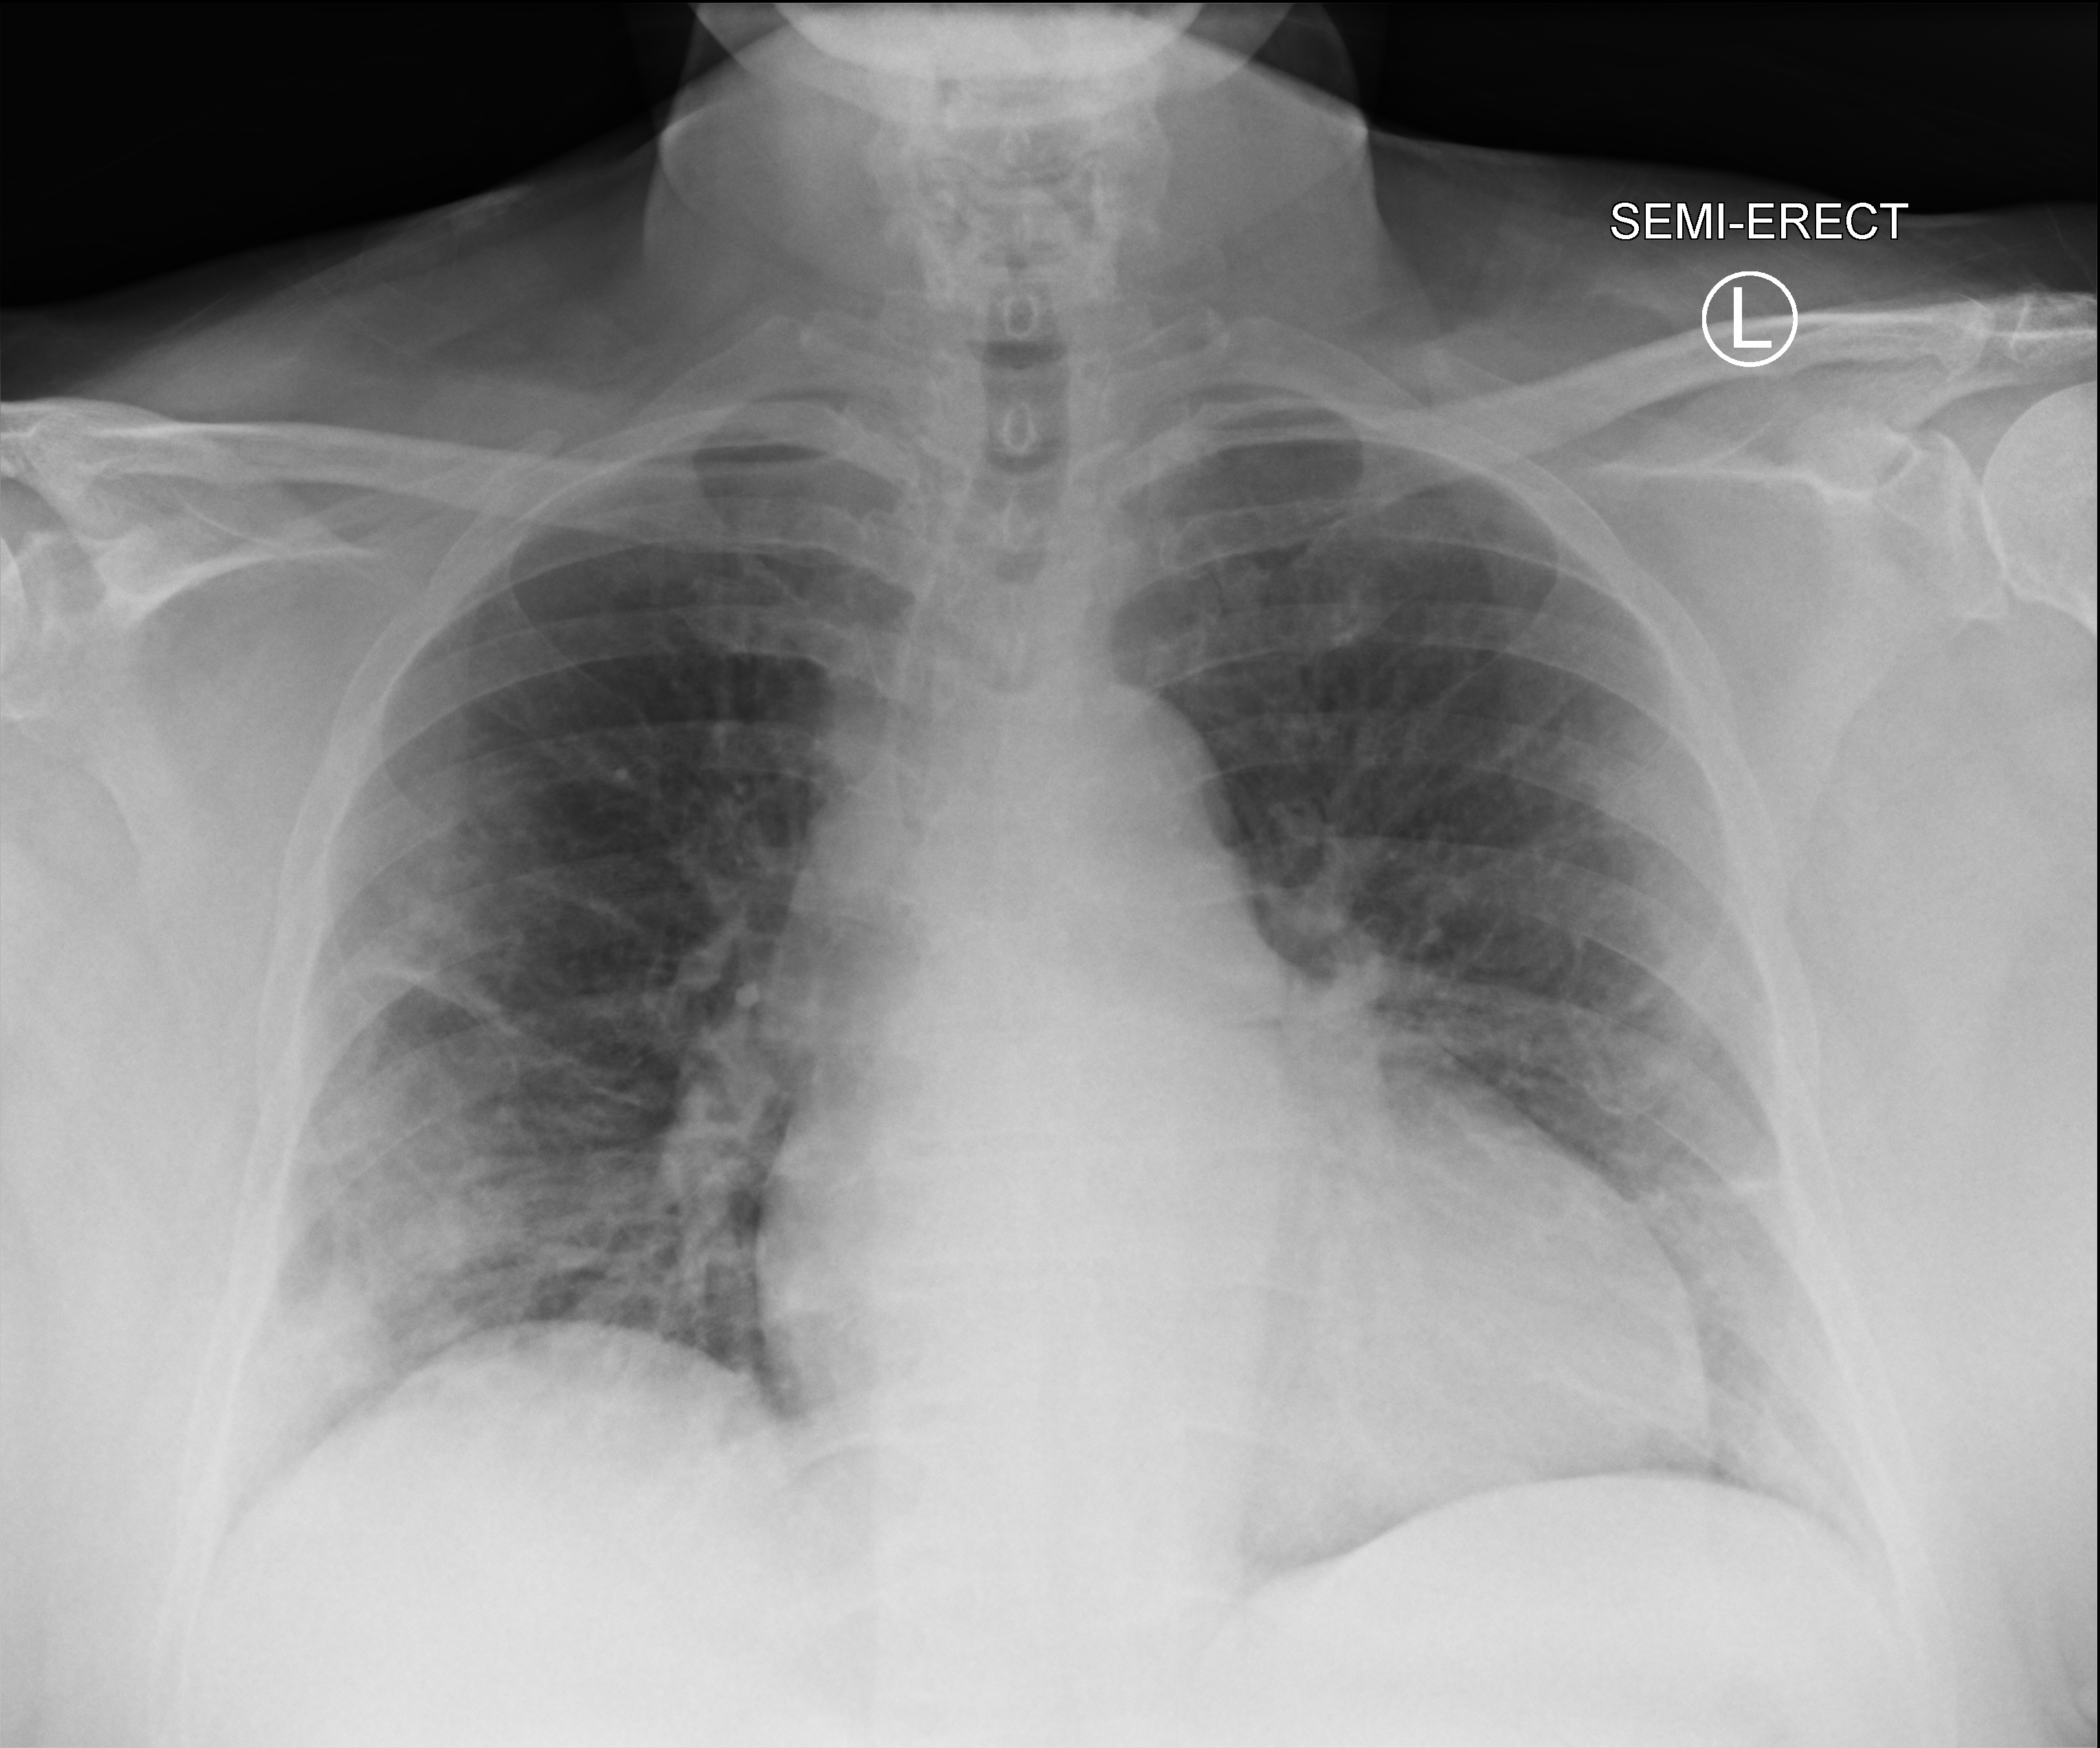
Portable chest radiograph; anteroposterior (AP) projection. Female patient hospitalised with COVID-19, age 60–74 years.
Admission-level facts for this patient (not findings on this image; timing relative to this image not recorded): length of hospital stay: 7 days; COPD (admission record): no; mechanically ventilated during this hospital stay: no.